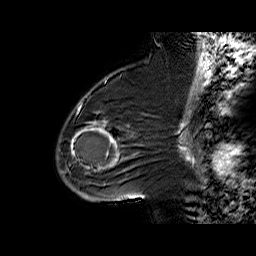
Breast MRI (dynamic contrast-enhanced), one sagittal slice; slice 39 of 60 in the series (ordered by position); dynamic contrast-enhanced series, time point 2 of 6 at this slice position (early post-contrast); 1.5 T; TE 6.3 ms, TR 32.4 ms; 4 mm slice thickness; 256 × 256 image matrix, field of view 200 × 200 mm. Female patient. Case-level facts recorded for this patient, not image findings: setting: breast cancer imaged before/during neoadjuvant chemotherapy; receptor status: triple-negative.
Structures marked on this image (semi-automatic segmentation, software-assisted and operator-edited):
- analysis volume of interest (the breast-tissue region the enhancement analysis was run in; not a lesion): bounding box [x1, y1, x2, y2] px = [65, 88, 140, 187]
- tumour enhancement mask (voxels above the 100 % enhancement threshold inside the analysis volume of interest): [70, 121, 117, 167]